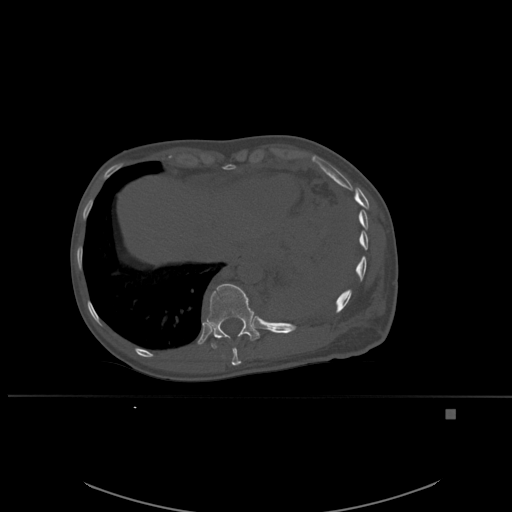
CT including the spine, one axial slice; slice 305 of 537 in the series (ordered by position); bone window (W 1800 / L 400 HU); 1.5 mm slice thickness; 512 × 512 image matrix, field of view 440 × 440 mm. Female patient, age 45 years. Case-level facts recorded for this patient, not image findings: primary cancer: lung.
Structures marked on this image (semi-automatic segmentation, software-assisted and operator-edited):
- T10 vertebra: bounding box <231,338,251,366> (left, top, right, bottom; pixels)
- T11 vertebra: <206,284,260,349>